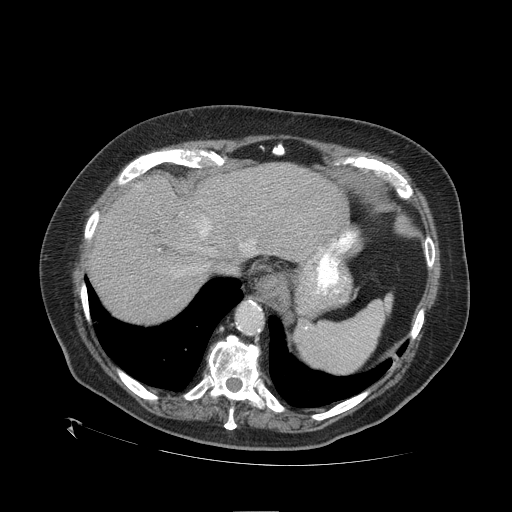
Contrast-enhanced abdominal CT (liver protocol), one axial slice; position 88 of 109 along the scan axis; reconstruction kernel STANDARD; one of 2 acquisitions stored at this slice position; soft-tissue window (W 400 / L 40 HU); 2.5 mm slice thickness; 512 × 512 image matrix. Case-level facts recorded for this patient, not image findings: diagnosis: hepatocellular carcinoma (patient treated with transarterial chemoembolisation; whether this scan precedes or follows treatment is not stated here); TNM stage (as recorded): Stage-I; Child-Pugh class: A; tumour differentiation: no biopsy; tumour nodularity: uninodular.
Structures marked on this image (semi-automatically segmented with operator editing):
- abdominal aorta: box from (x=238, y=303) to (x=263, y=333) px
- liver parenchyma outside the tumour (the mass and vessels are separate outlines, so this box may not span the whole liver): (x=88, y=162)–(x=348, y=322)
- mass: (x=174, y=203)–(x=210, y=245)
- liver vessels: (x=240, y=242)–(x=322, y=251)